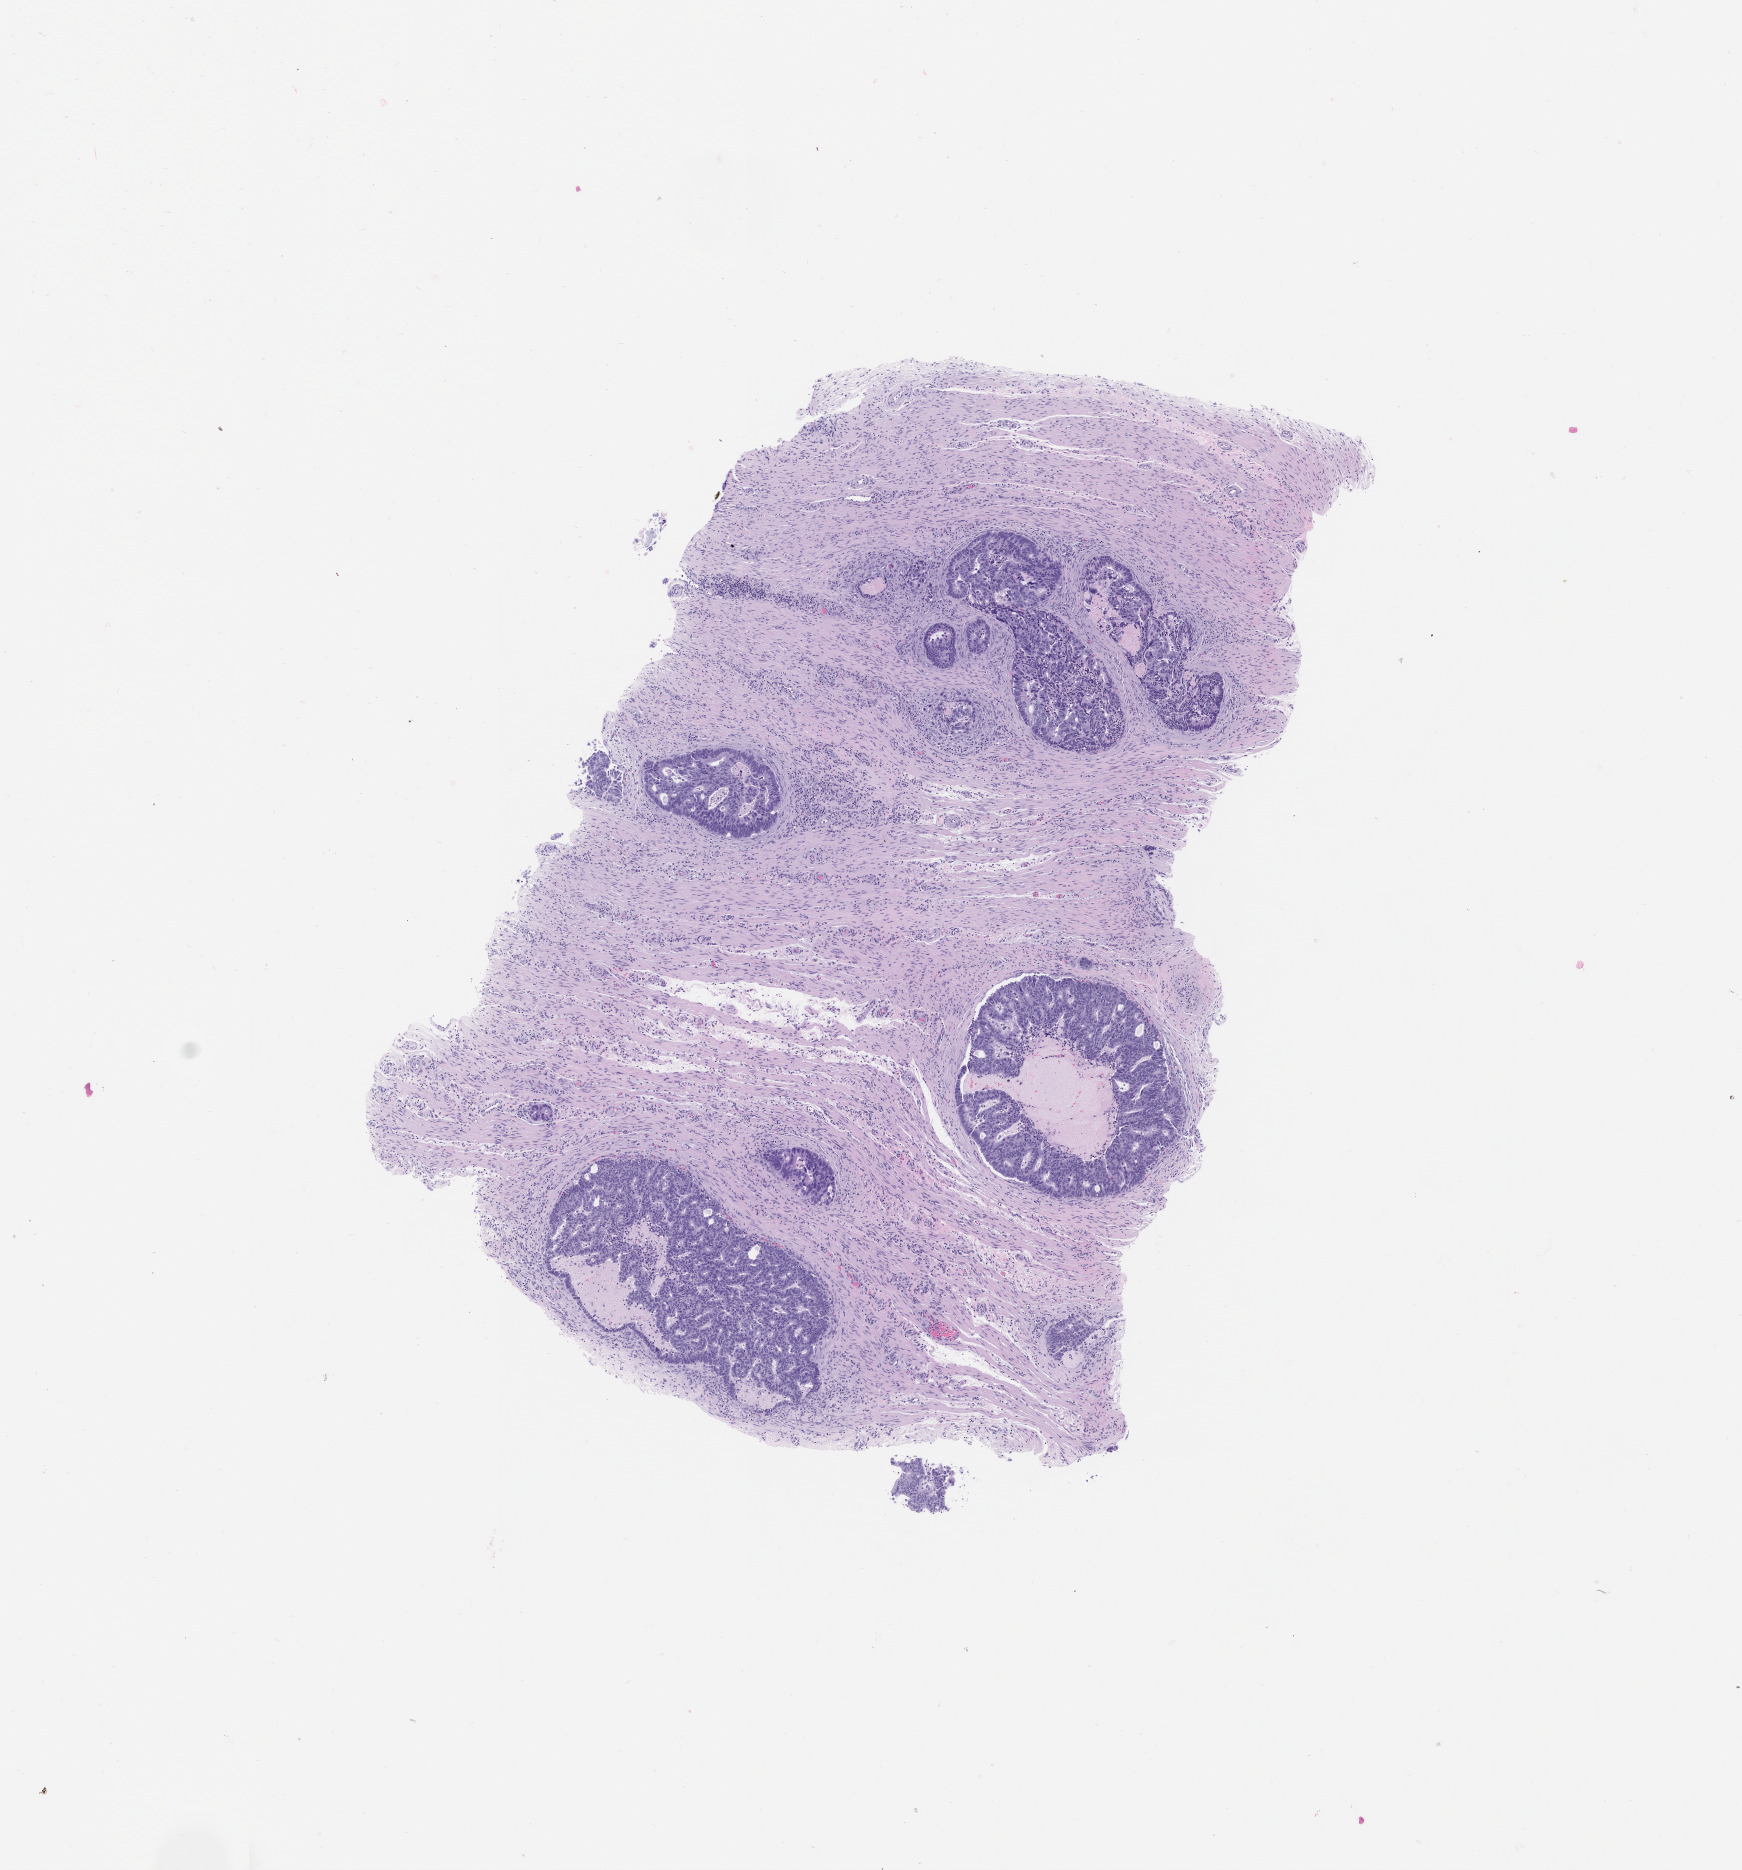
Digitized haematoxylin and eosin-stained section of the patient's (originator) tumor tissue, whole scanned area (about 7.0 x 7.5 mm) shown as a low-resolution overview; formalin-fixed, paraffin-embedded (FFPE) tissue; originating tumor site category: colon. Patient: male, age 79 years.
• diagnosis: Colon Adenocarcinoma